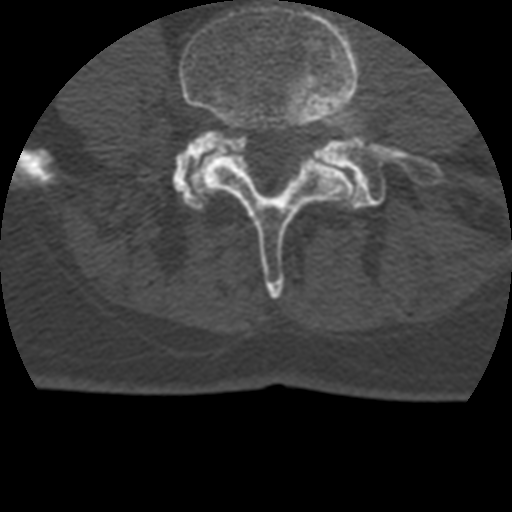
CT including the spine, one axial slice; position 58 of 399 along the scan axis; reconstruction kernel STANDARD; bone window (W 1800 / L 400 HU); 1.25 mm slice thickness; 512 × 512 image matrix, field of view 160 × 160 mm. Patient age 69 years. From the clinical record (not read from this slice): primary cancer: prostate.
Annotated regions visible in this slice (semi-automatically segmented with operator editing):
- L4 vertebra: bounding box (x1, y1, x2, y2) in pixels: (179, 2, 362, 299)
- L5 vertebra: (172, 116, 432, 210)